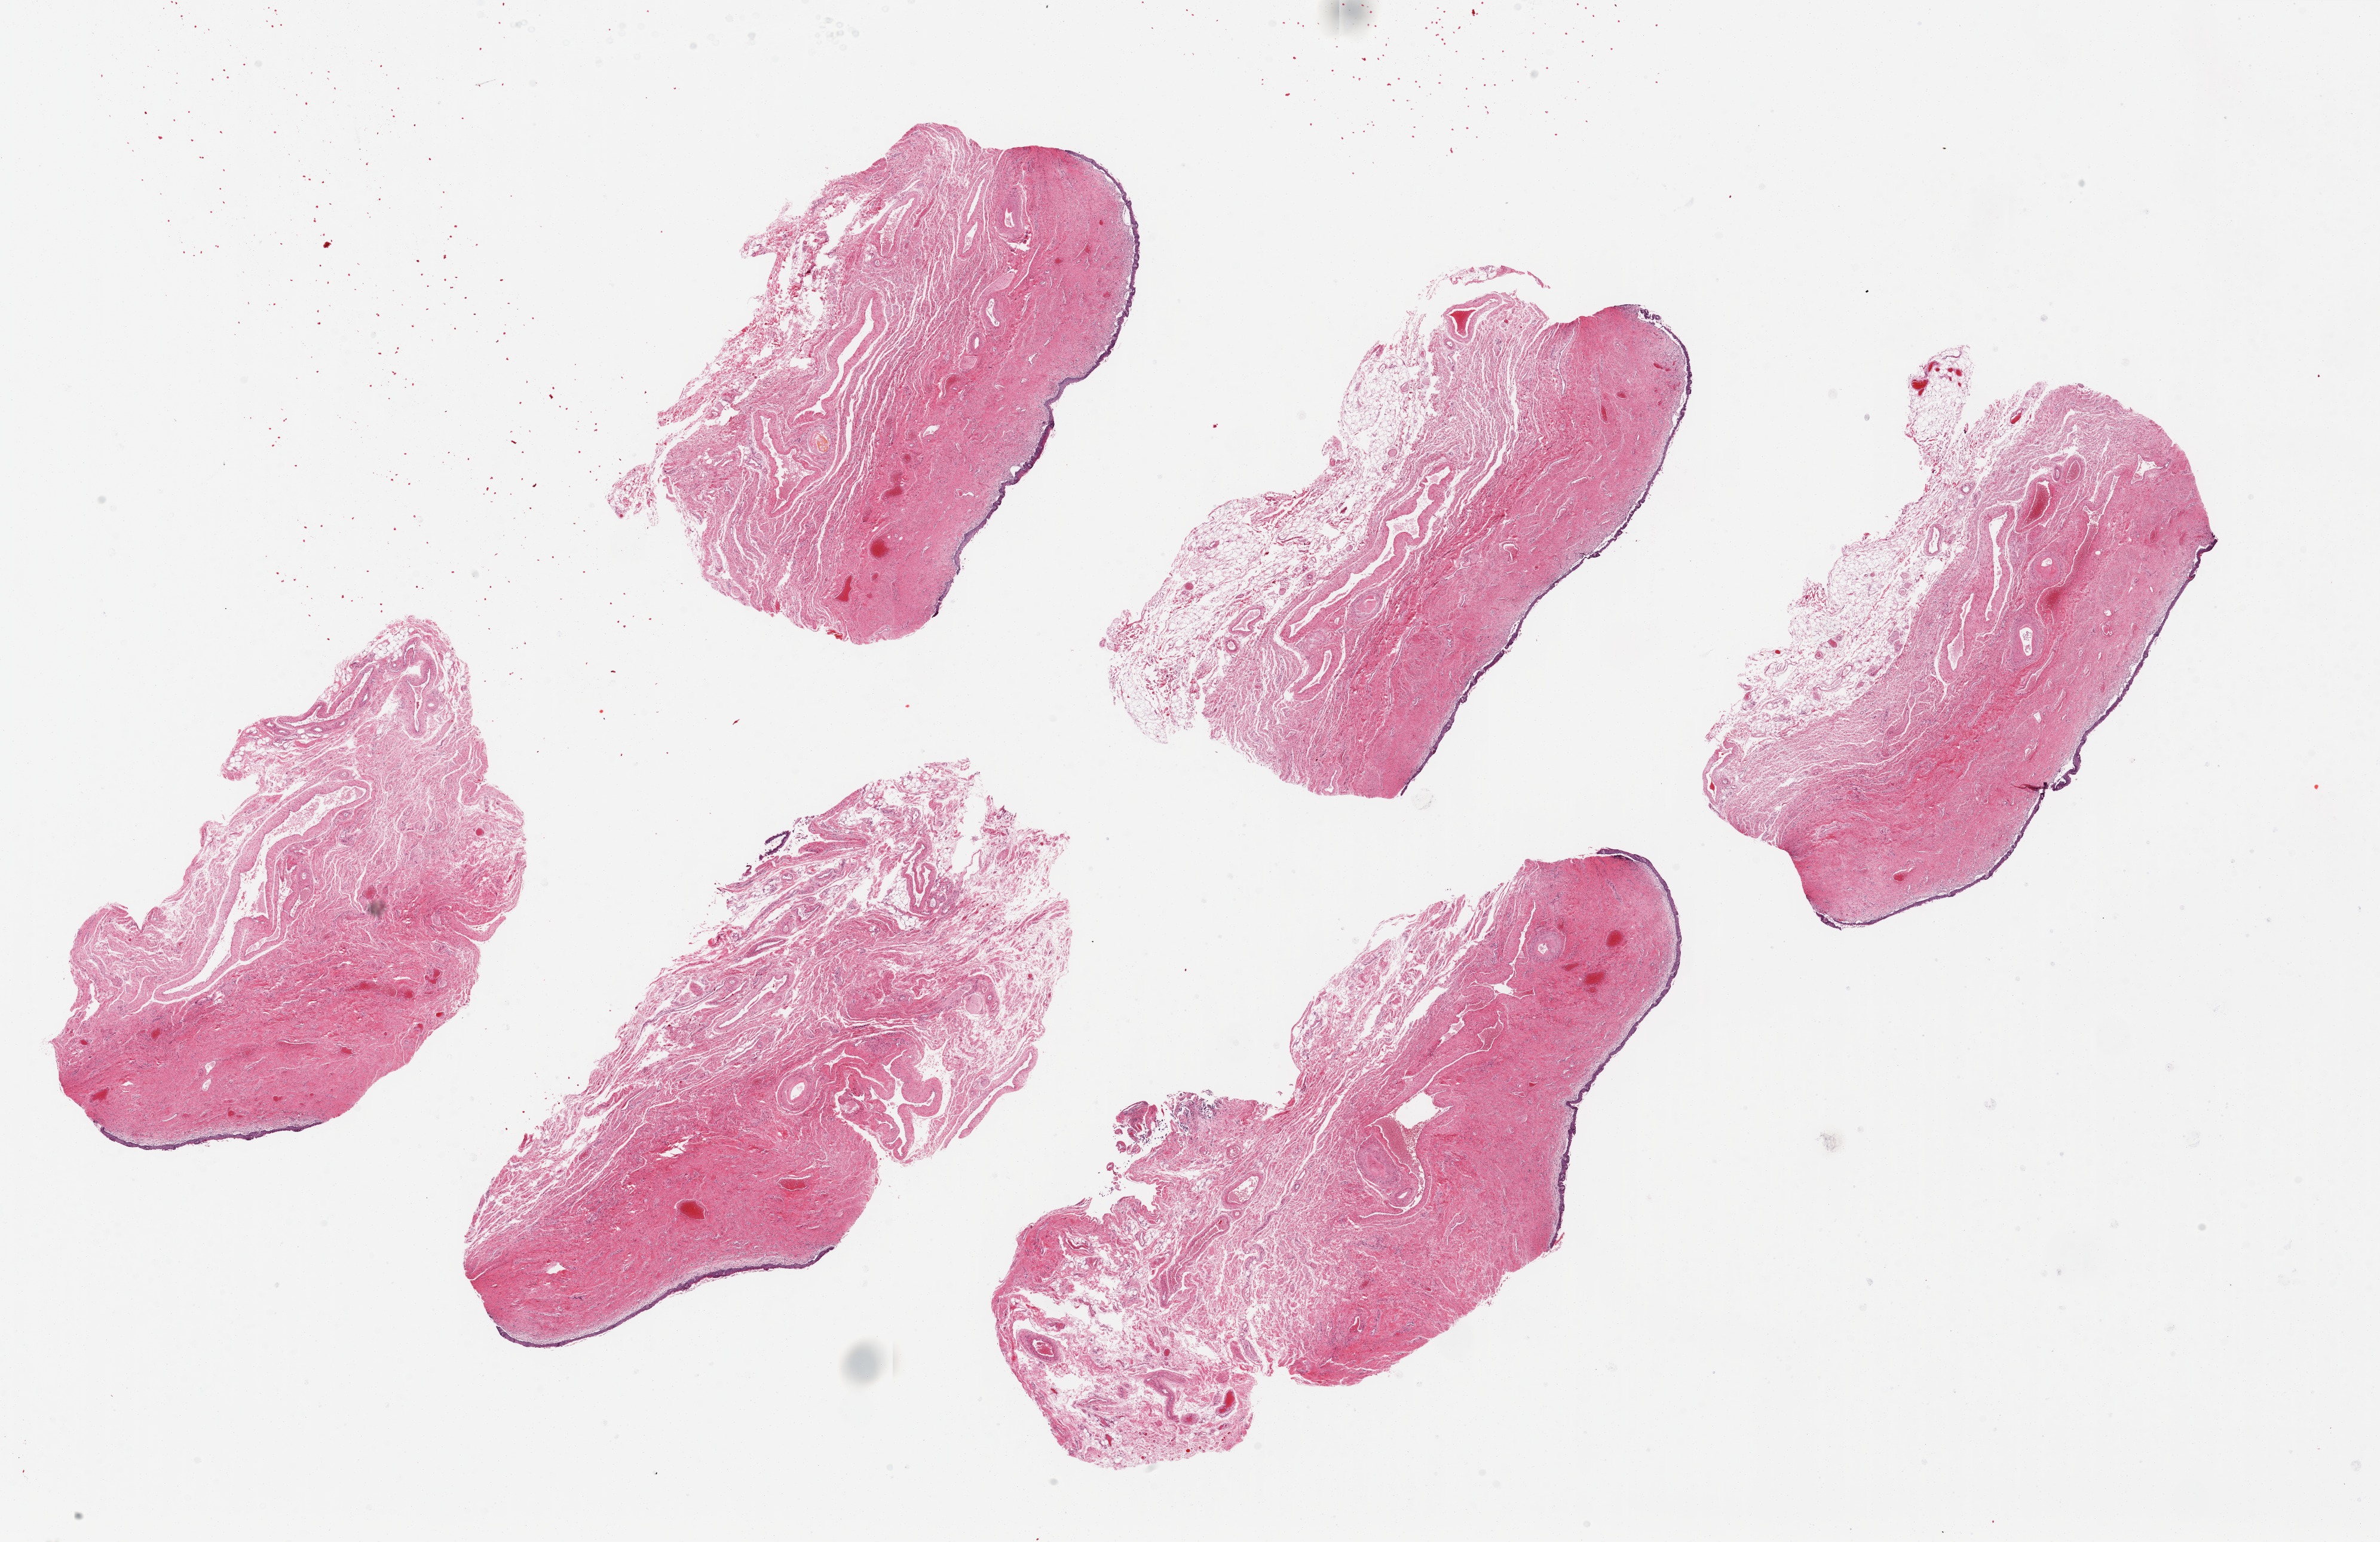
Whole-slide image, hematoxylin and eosin (H&E) stain, whole scanned area (about 31.5 x 20.4 mm) shown as a low-resolution overview; PAXgene-fixed, paraffin-embedded tissue; sampled site (target tissue): vagina; tissue donor sample. Donor: female.
Pathologist's review note for this sample: 6 pieces up to 10x4.3 mm; mucosa partly sloughed and detached.